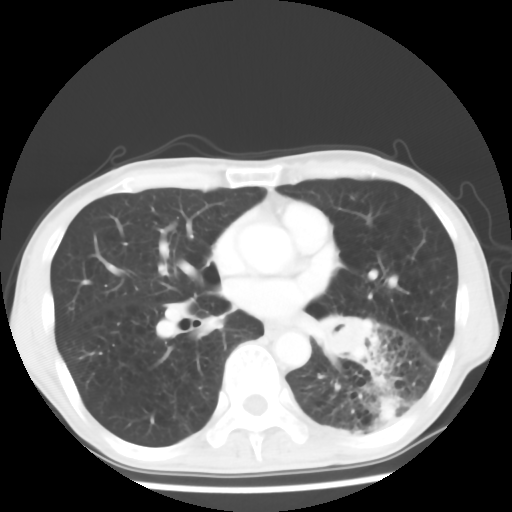
Chest CT, one axial slice. Slice 30 of 64 in the series (ordered by position). 120 kVp. Lung window (W 1500 / L -600 HU). 5 mm slice thickness. 512 × 512 image matrix, field of view 313 × 313 mm. Male patient, age 68 years. From the clinical record (not read from this slice): clinical TNM (as recorded): T4 N0 M0.
Outlined on this slice (bounding box drawn by a radiologist):
- lung tumour (recorded histology: squamous cell carcinoma): bounding box (x1, y1, x2, y2) in pixels: (313, 303, 387, 372)